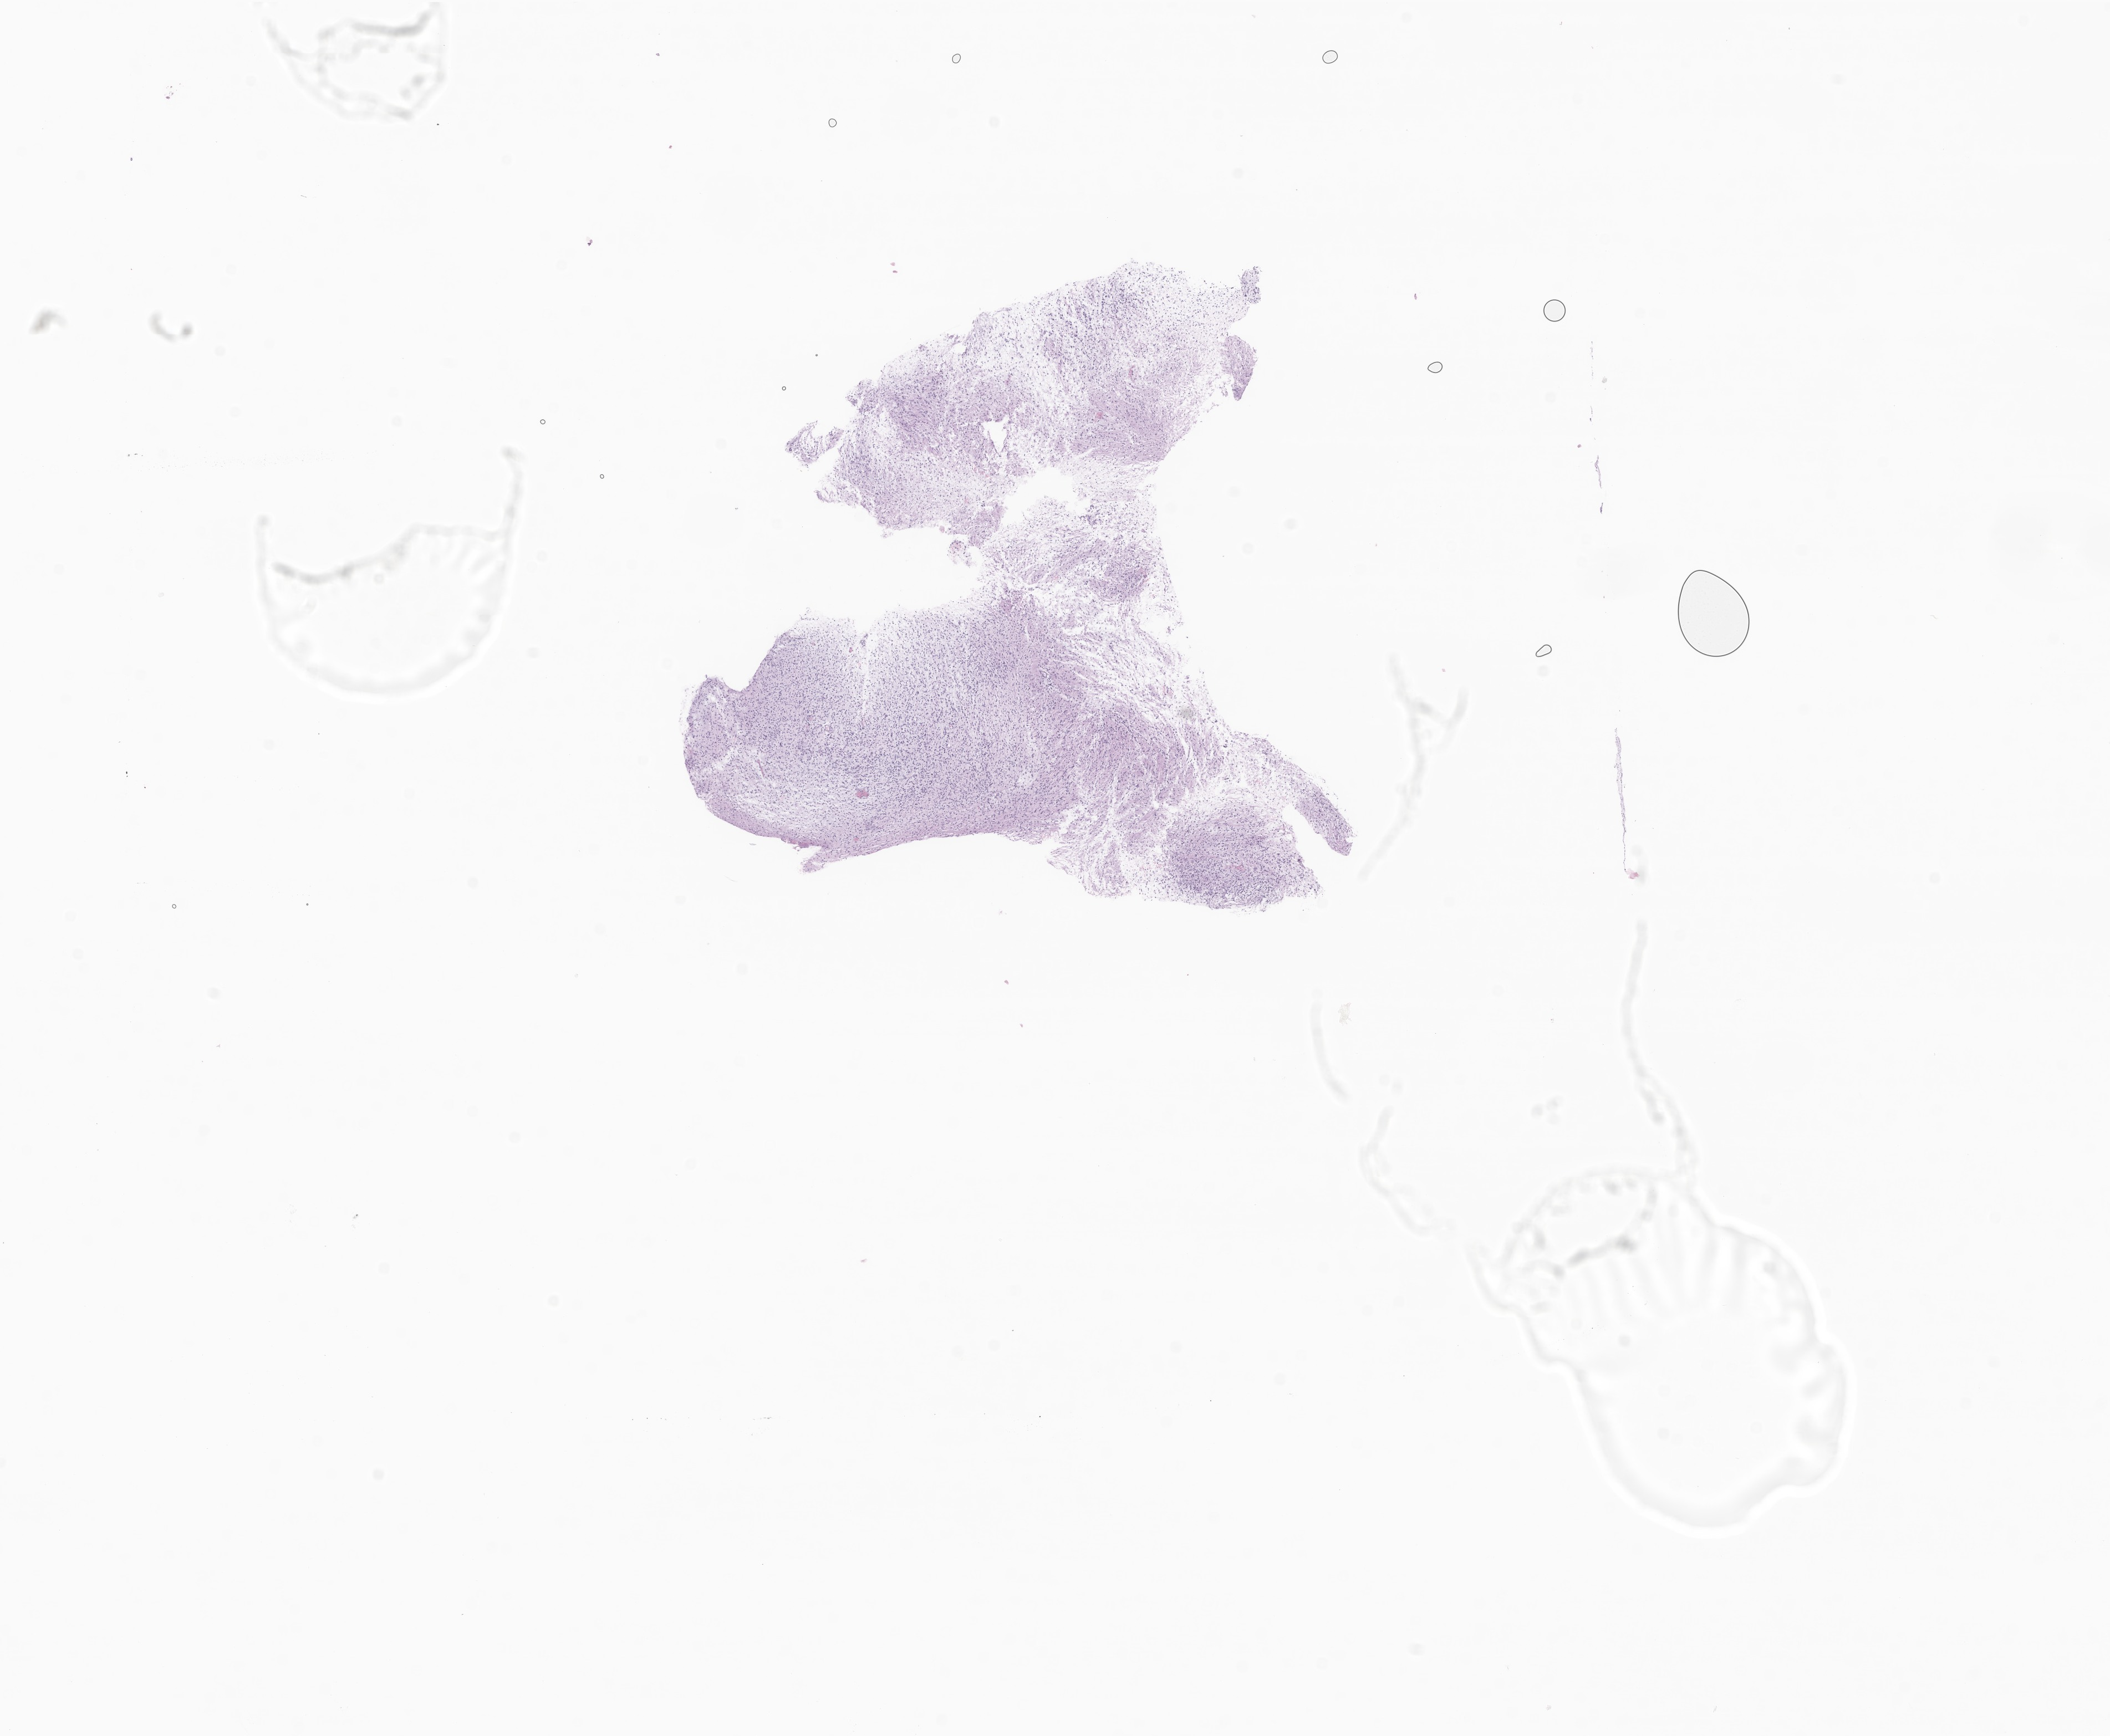
H&E whole-slide image of tumor tissue from the brain — whole scanned area (about 16.0 x 13.2 mm) shown as a low-resolution overview. FFPE section. Patient: female, age 104 months (8 years 8 months).
- diagnosis (ICD-O-3 morphology term): Glioma, malignant